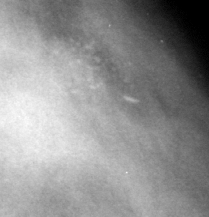
Cropped region of a digitized screen-film mammogram centred on a radiologist-marked abnormality, left breast, MLO view.
Marked abnormality: calcifications, morphology pleomorphic, distribution clustered; BI-RADS assessment category 4; pathology result (as recorded, not read from the image): benign.